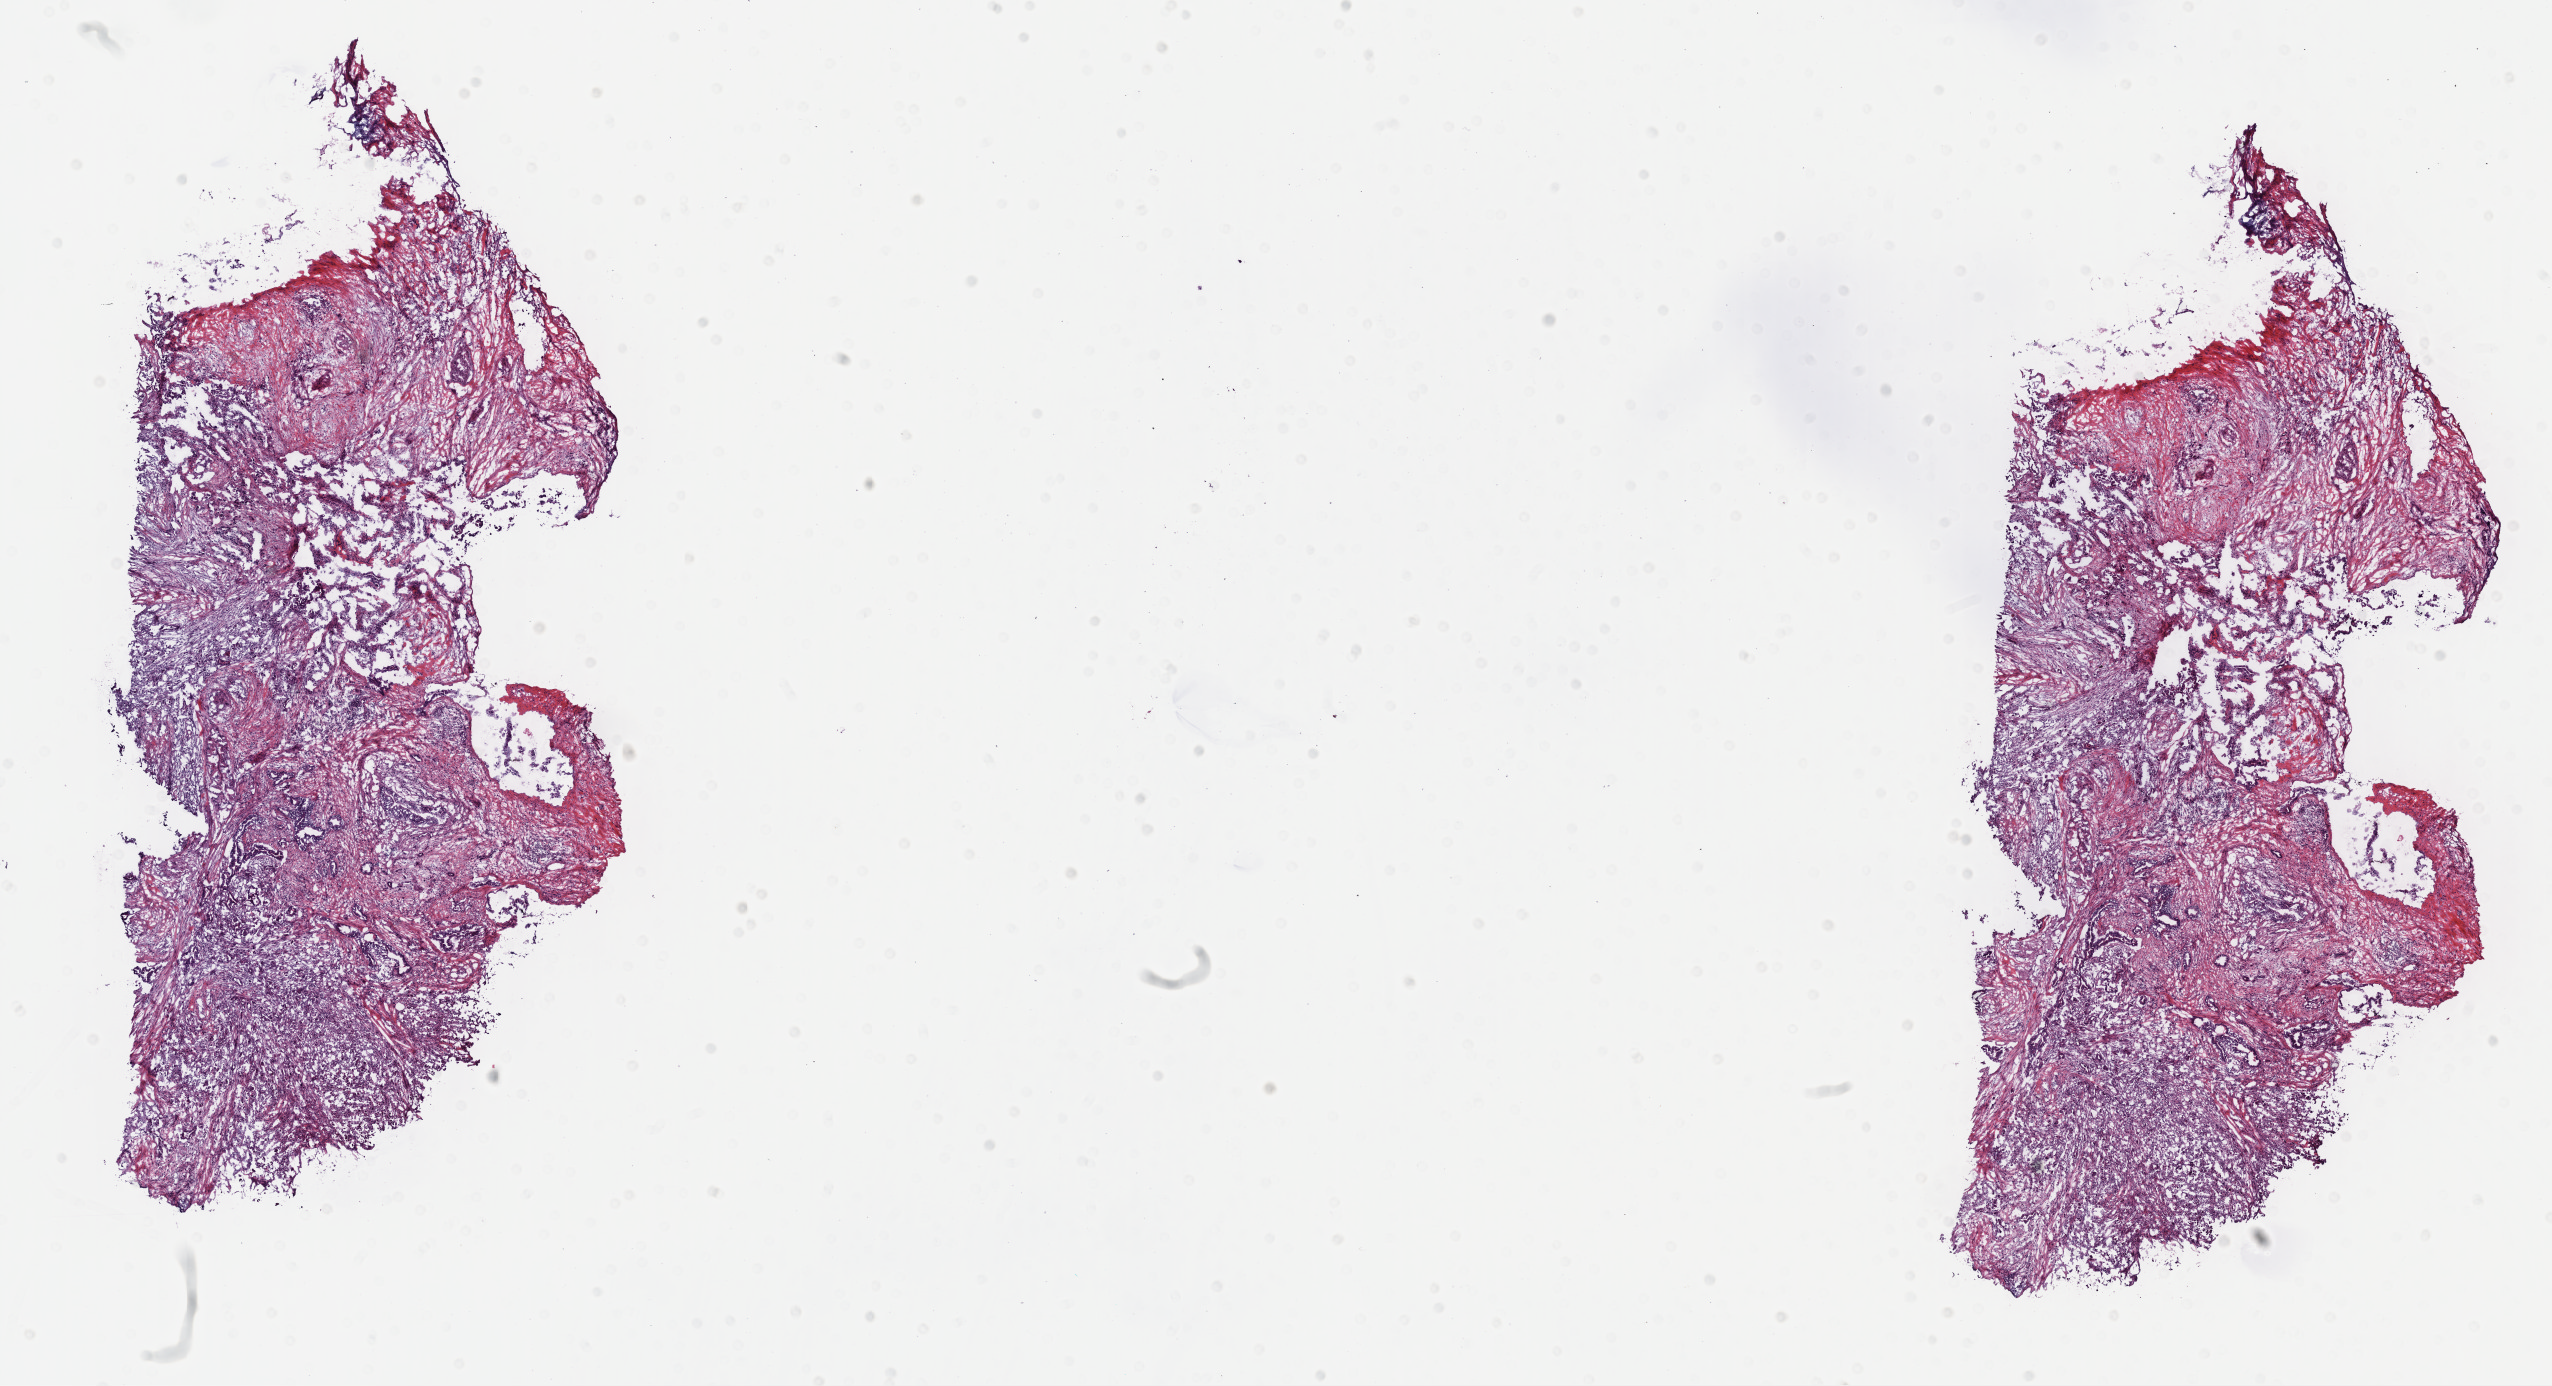
H&E-stained whole-slide image — low-resolution overview of the scanned area, about 20.6 x 11.2 mm (slide scanned at 40x), frozen section, pancreas, primary tumour sample. Patient: female, age at initial diagnosis 62 years. Histologic grade: G2 (moderately differentiated). Pathologist review of this section (percent, as recorded): tumour cells 70%, tumour nuclei 70%, normal cells 0%, stromal cells 30%, necrosis 0%. Infiltration values recorded for this section: lymphocyte infiltration 70%, monocyte infiltration 10%, neutrophil infiltration 10%.
Pathologic diagnosis: Infiltrating duct carcinoma, NOS (head of pancreas). AJCC pathologic stage: IIB (7th edition). TNM: T2 N1 MX.